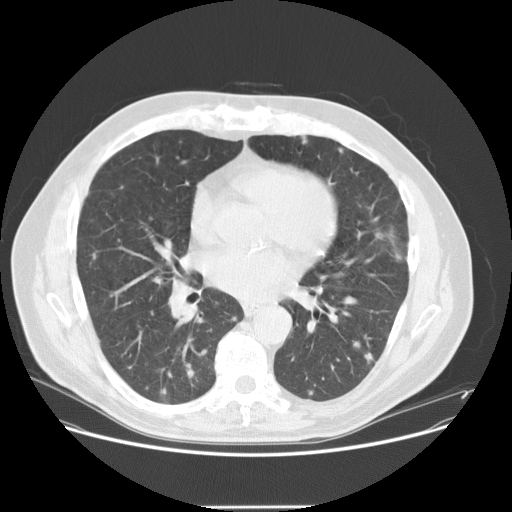
Low-dose screening chest CT, one axial slice; position 70 of 143 along the scan axis; reconstruction kernel STANDARD; lung window (W 1500 / L -600 HU); 512 × 512 image matrix.
Annotated regions visible in this slice (expert manual segmentation):
- lesion 7 (tumor): bounding box <364,352,374,364> (left, top, right, bottom; pixels)